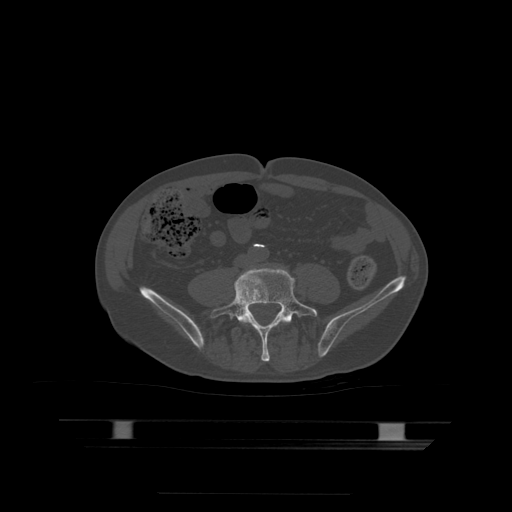
CT including the spine, one axial slice; slice 77 of 522 in the series (ordered by position); bone window (W 1800 / L 400 HU); 1.25 mm slice thickness; 512 × 512 image matrix, field of view 436 × 436 mm. Patient age 68 years. From the clinical record (not read from this slice): primary cancer: urothelial.
Annotated regions visible in this slice (semi-automatic segmentation, software-assisted and operator-edited):
- L4 vertebra: bounding box <242,318,290,324> (left, top, right, bottom; pixels)
- L5 vertebra: <210,269,318,362>